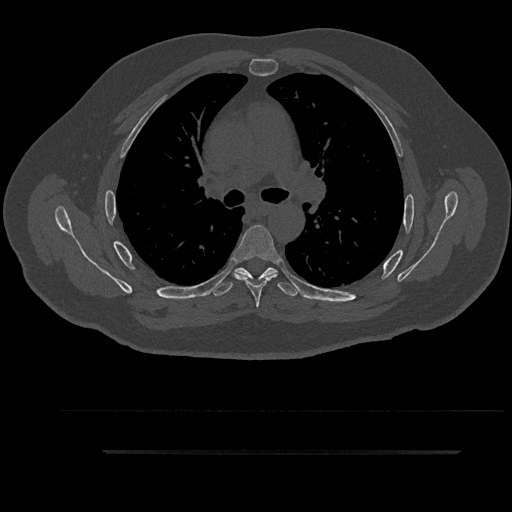
CT including the spine, one axial slice; position 611 of 797 along the scan axis; bone window (W 1800 / L 400 HU); 0.5 mm slice thickness; 512 × 512 image matrix, field of view 432 × 432 mm. Male patient, age 63 years. From the clinical record (not read from this slice): primary cancer: renal; vertebrae with lytic lesions (as recorded): T8.
Annotated regions visible in this slice (semi-automatic segmentation, software-assisted and operator-edited):
- T5 vertebra: box from (x=232, y=225) to (x=282, y=308) px
- T6 vertebra: (x=212, y=267)–(x=299, y=296)